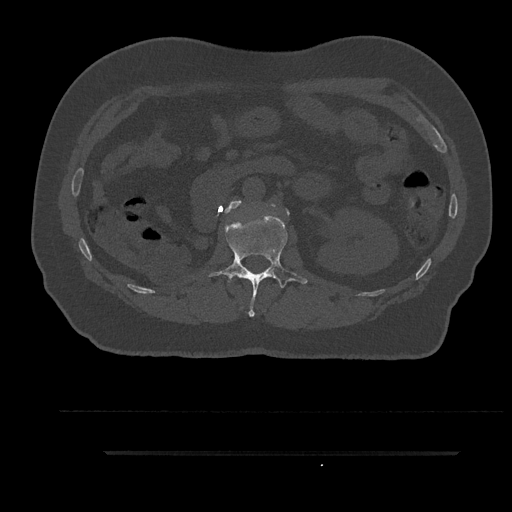
CT including the spine, one axial slice. Position 168 of 797 along the scan axis. Reconstruction kernel Br40s/3. Bone window (W 1800 / L 400 HU). 0.5 mm slice thickness. 512 × 512 image matrix, field of view 432 × 432 mm. Male patient, age 63 years. Case-level facts recorded for this patient, not image findings: primary cancer: renal; vertebrae with lytic lesions (as recorded): T8.
Structures marked on this image (semi-automatic segmentation, software-assisted and operator-edited):
- L1 vertebra: bounding box (x1, y1, x2, y2) in pixels: (208, 215, 308, 317)
- L2 vertebra: (225, 200, 289, 216)